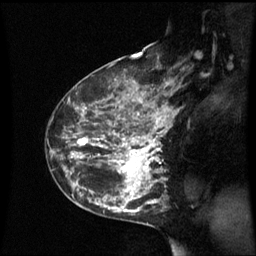
Breast MRI (dynamic contrast-enhanced), one sagittal slice. Slice 37 of 60 in the series (ordered by position). Dynamic contrast-enhanced series, image 2 of 3 at this slice position (ordered by acquisition). 1.5 T. TE 4.2 ms, TR 8.9 ms. 256 × 256 image matrix, field of view 210 × 210 mm. Female patient, age 42 years. Case-level facts recorded for this patient, not image findings: setting: breast cancer imaged before/during neoadjuvant chemotherapy; receptor status: HER2-positive.
Structures marked on this image (semi-automatically segmented with operator editing):
- analysis volume of interest (the breast-tissue region the enhancement analysis was run in; not a lesion): bounding box <62,93,171,210> (left, top, right, bottom; pixels)
- tumour enhancement mask (voxels above the 70 % enhancement threshold inside the analysis volume of interest): <73,99,171,210>